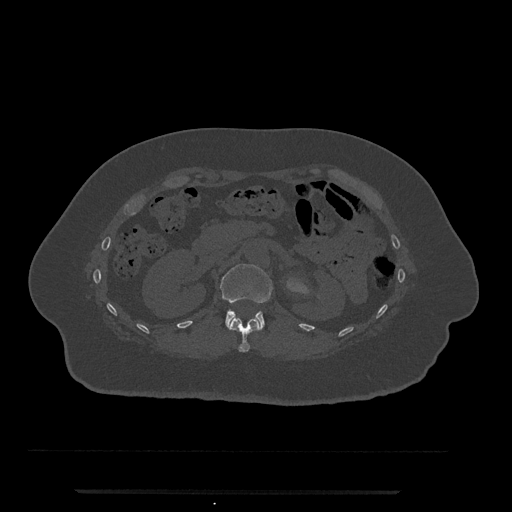
CT including the spine, one axial slice; reconstruction kernel Br40s/3; 120 kVp; bone window (W 1800 / L 400 HU); 0.5 mm slice thickness; 512 × 512 image matrix, field of view 440 × 440 mm. Female patient, age 51 years. From the clinical record (not read from this slice): primary cancer: neuro.
Structures marked on this image (semi-automatically segmented with operator editing):
- L1 vertebra: bounding box <220,264,273,329> (left, top, right, bottom; pixels)
- T12 vertebra: <228,317,261,353>